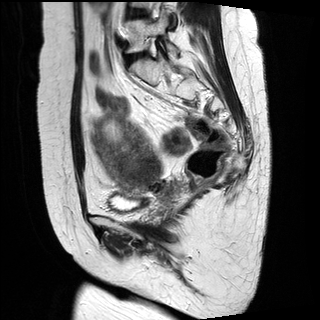
Pelvic MRI for cervical cancer, one sagittal slice; slice 12 of 29 in the series (ordered by position); T2-weighted; 1.5 T; TE 89 ms, TR 2930 ms; 4 mm slice thickness; 320 × 320 image matrix. Female patient, age 49 years.
Annotated regions visible in this slice (expert manual segmentation):
- uterus and cervix: bounding box <91,113,161,194> (left, top, right, bottom; pixels)